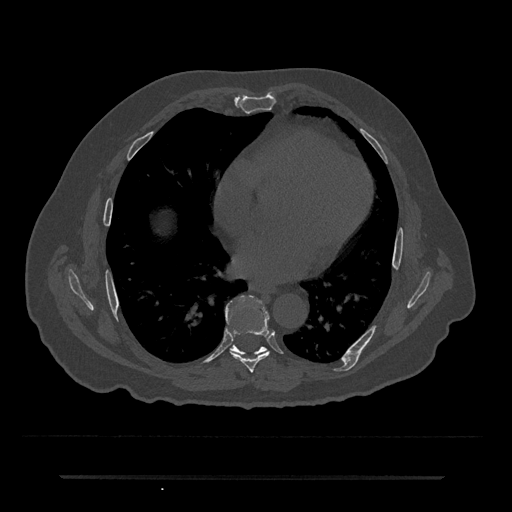
CT including the spine, one axial slice; slice 366 of 797 in the series (ordered by position); reconstruction kernel Br40s/3; 120 kVp; bone window (W 1800 / L 400 HU); 0.5 mm slice thickness; 512 × 512 image matrix, field of view 437 × 437 mm. Male patient, age 69 years. From the clinical record (not read from this slice): primary cancer: prostate.
Annotated regions visible in this slice (semi-automatic segmentation, software-assisted and operator-edited):
- T7 vertebra: bounding box <226,297,270,373> (left, top, right, bottom; pixels)
- T8 vertebra: <230,345,266,355>